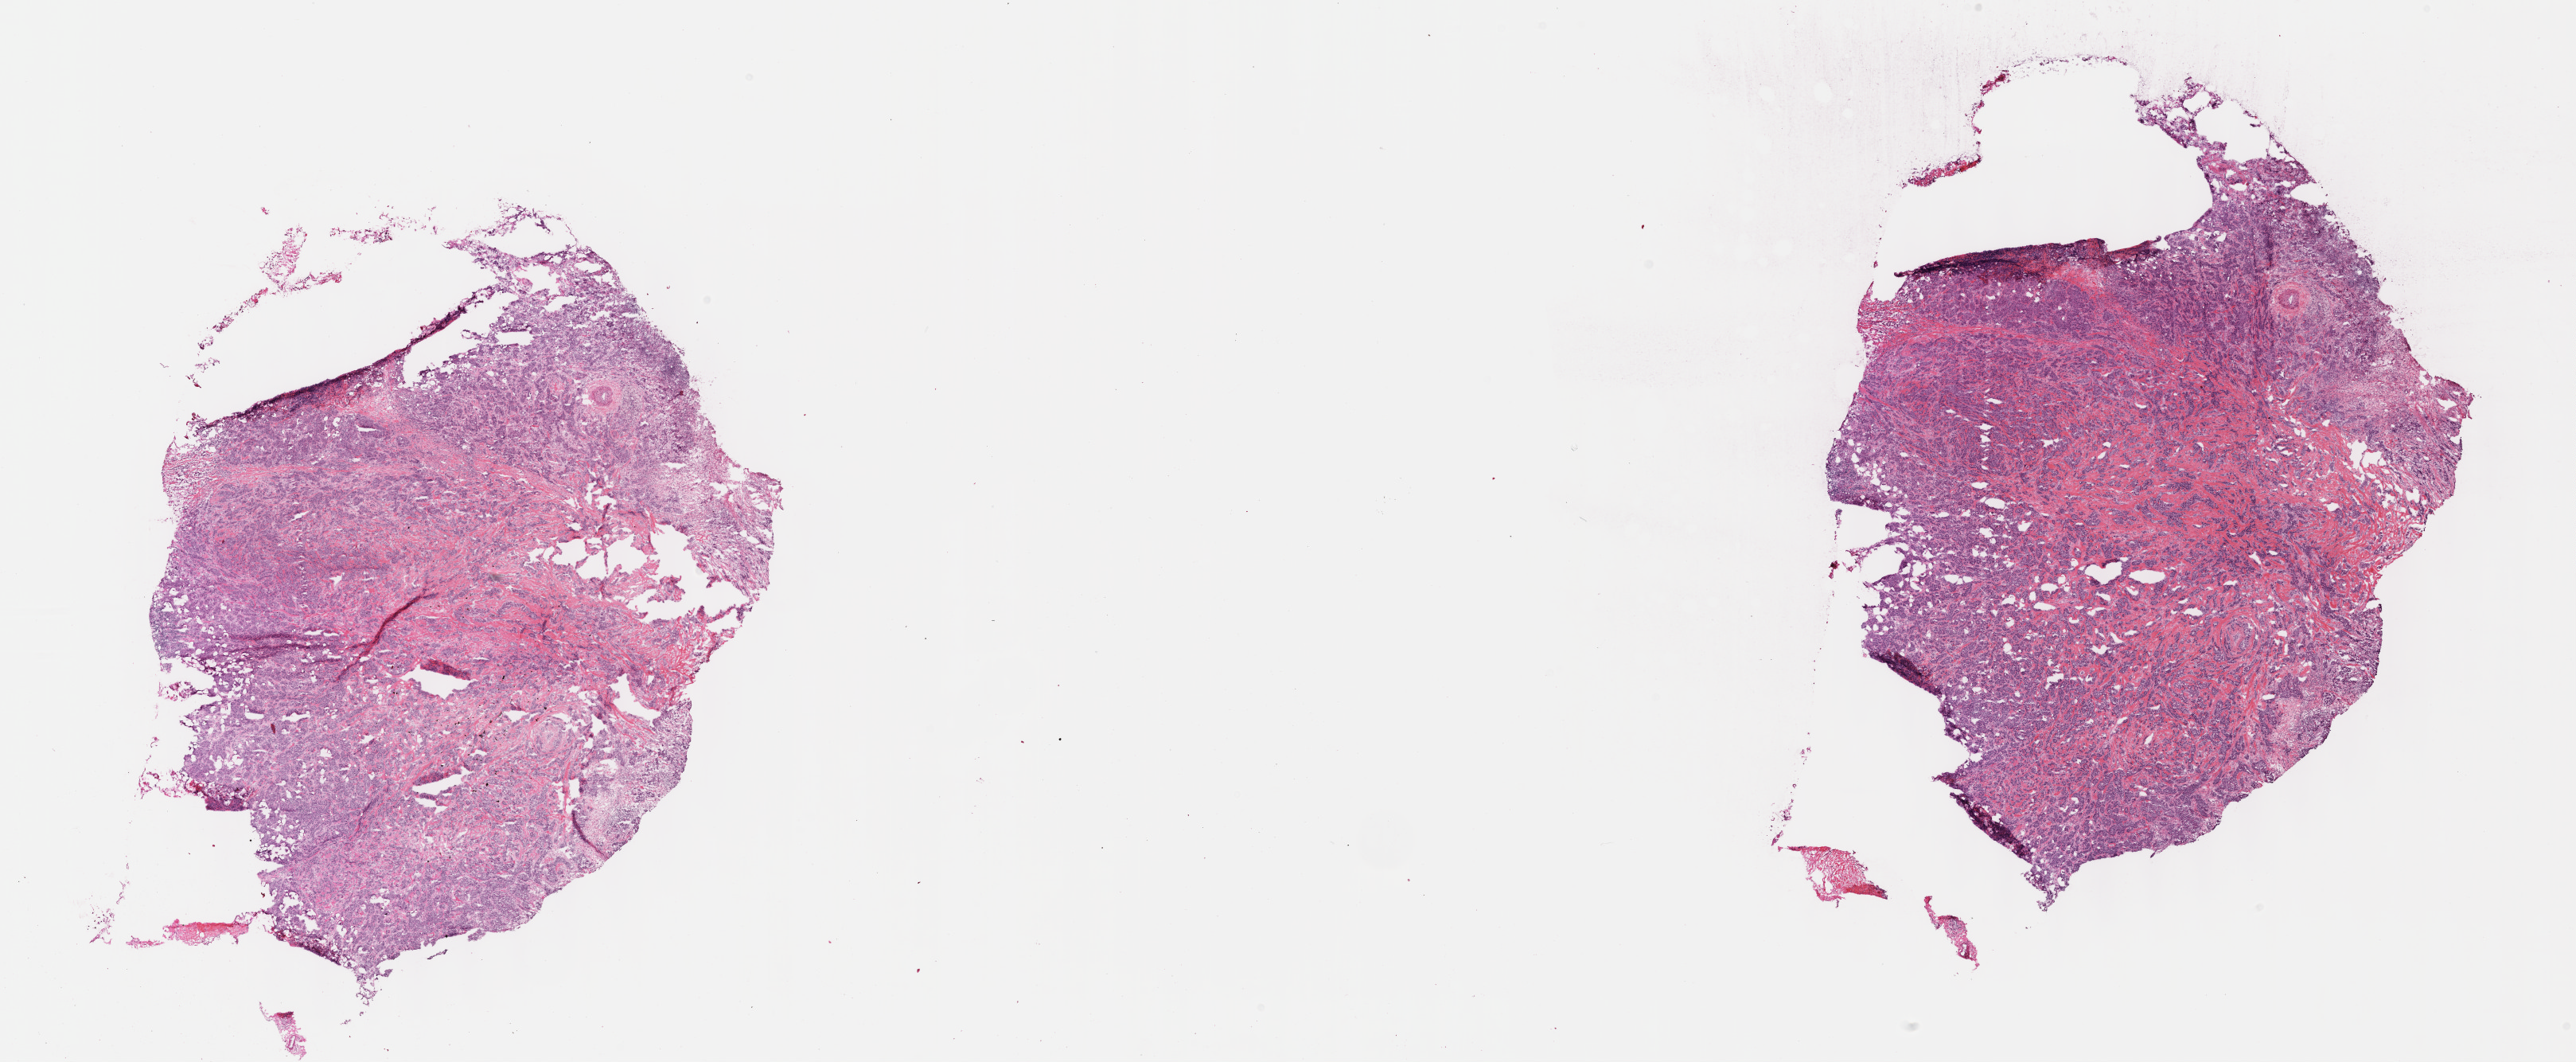
Whole-slide histology image, H&E-stained — shown as a low-resolution overview of the whole scanned area (about 26.2 x 10.8 mm, from a 40x scan); formalin-fixed paraffin-embedded (FFPE) diagnostic section; primary tumour sample from the breast. Female patient; age at initial diagnosis 68 years.
Pathologic diagnosis: Infiltrating duct carcinoma, NOS. AJCC pathologic stage: IIA. Lymph nodes positive (case pathology): 0 of 19 examined.